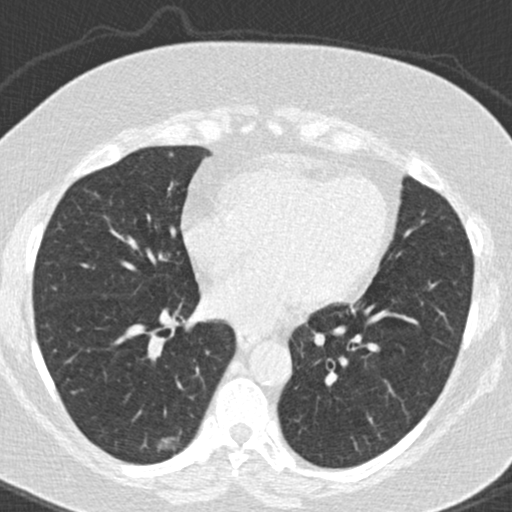
Chest CT (low-dose screening protocol), one axial image; first (baseline) screen; lung window (W 1500 / L -600 HU); 2 mm slice thickness; standard (soft-tissue) reconstruction kernel (B30f); 120 kVp. Female, age 63 years at enrolment. Former smoker at enrolment.
Expert reader's lesion annotation, box from (x=146, y=427) to (x=190, y=463) px. Screening reader's record for this exam (one nodule recorded; not confirmed to be the boxed lesion): non-calcified nodule or mass ≥4 mm, right lower lobe, 16 × 10 mm, poorly defined margins, ground glass attenuation. Later outcome: lung cancer diagnosed 246 days after this screen — bronchiolo-alveolar adenocarcinoma, NOS, right lower lobe, well differentiated (G1), stage IA (AJCC 6th edition), 12 mm at pathology.